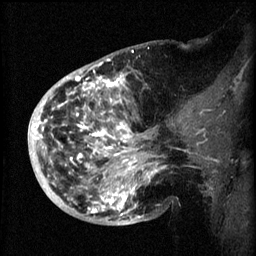
Breast MRI (dynamic contrast-enhanced), one sagittal slice; slice 22 of 60 in the series (ordered by position); 3 images stored at this slice position (order not interpretable as contrast timing); 1.5 T; TE 4.2 ms, TR 8.2 ms; 2 mm slice thickness; 256 × 256 image matrix. Female patient, age 50 years.
Annotated regions visible in this slice (semi-automatic segmentation, software-assisted and operator-edited):
- analysis volume of interest (the breast-tissue region the enhancement analysis was run in; not a lesion): bounding box (x1, y1, x2, y2) in pixels: (44, 72, 172, 219)
- tumour enhancement mask (voxels above the 70 % enhancement threshold inside the analysis volume of interest): (44, 76, 160, 219)